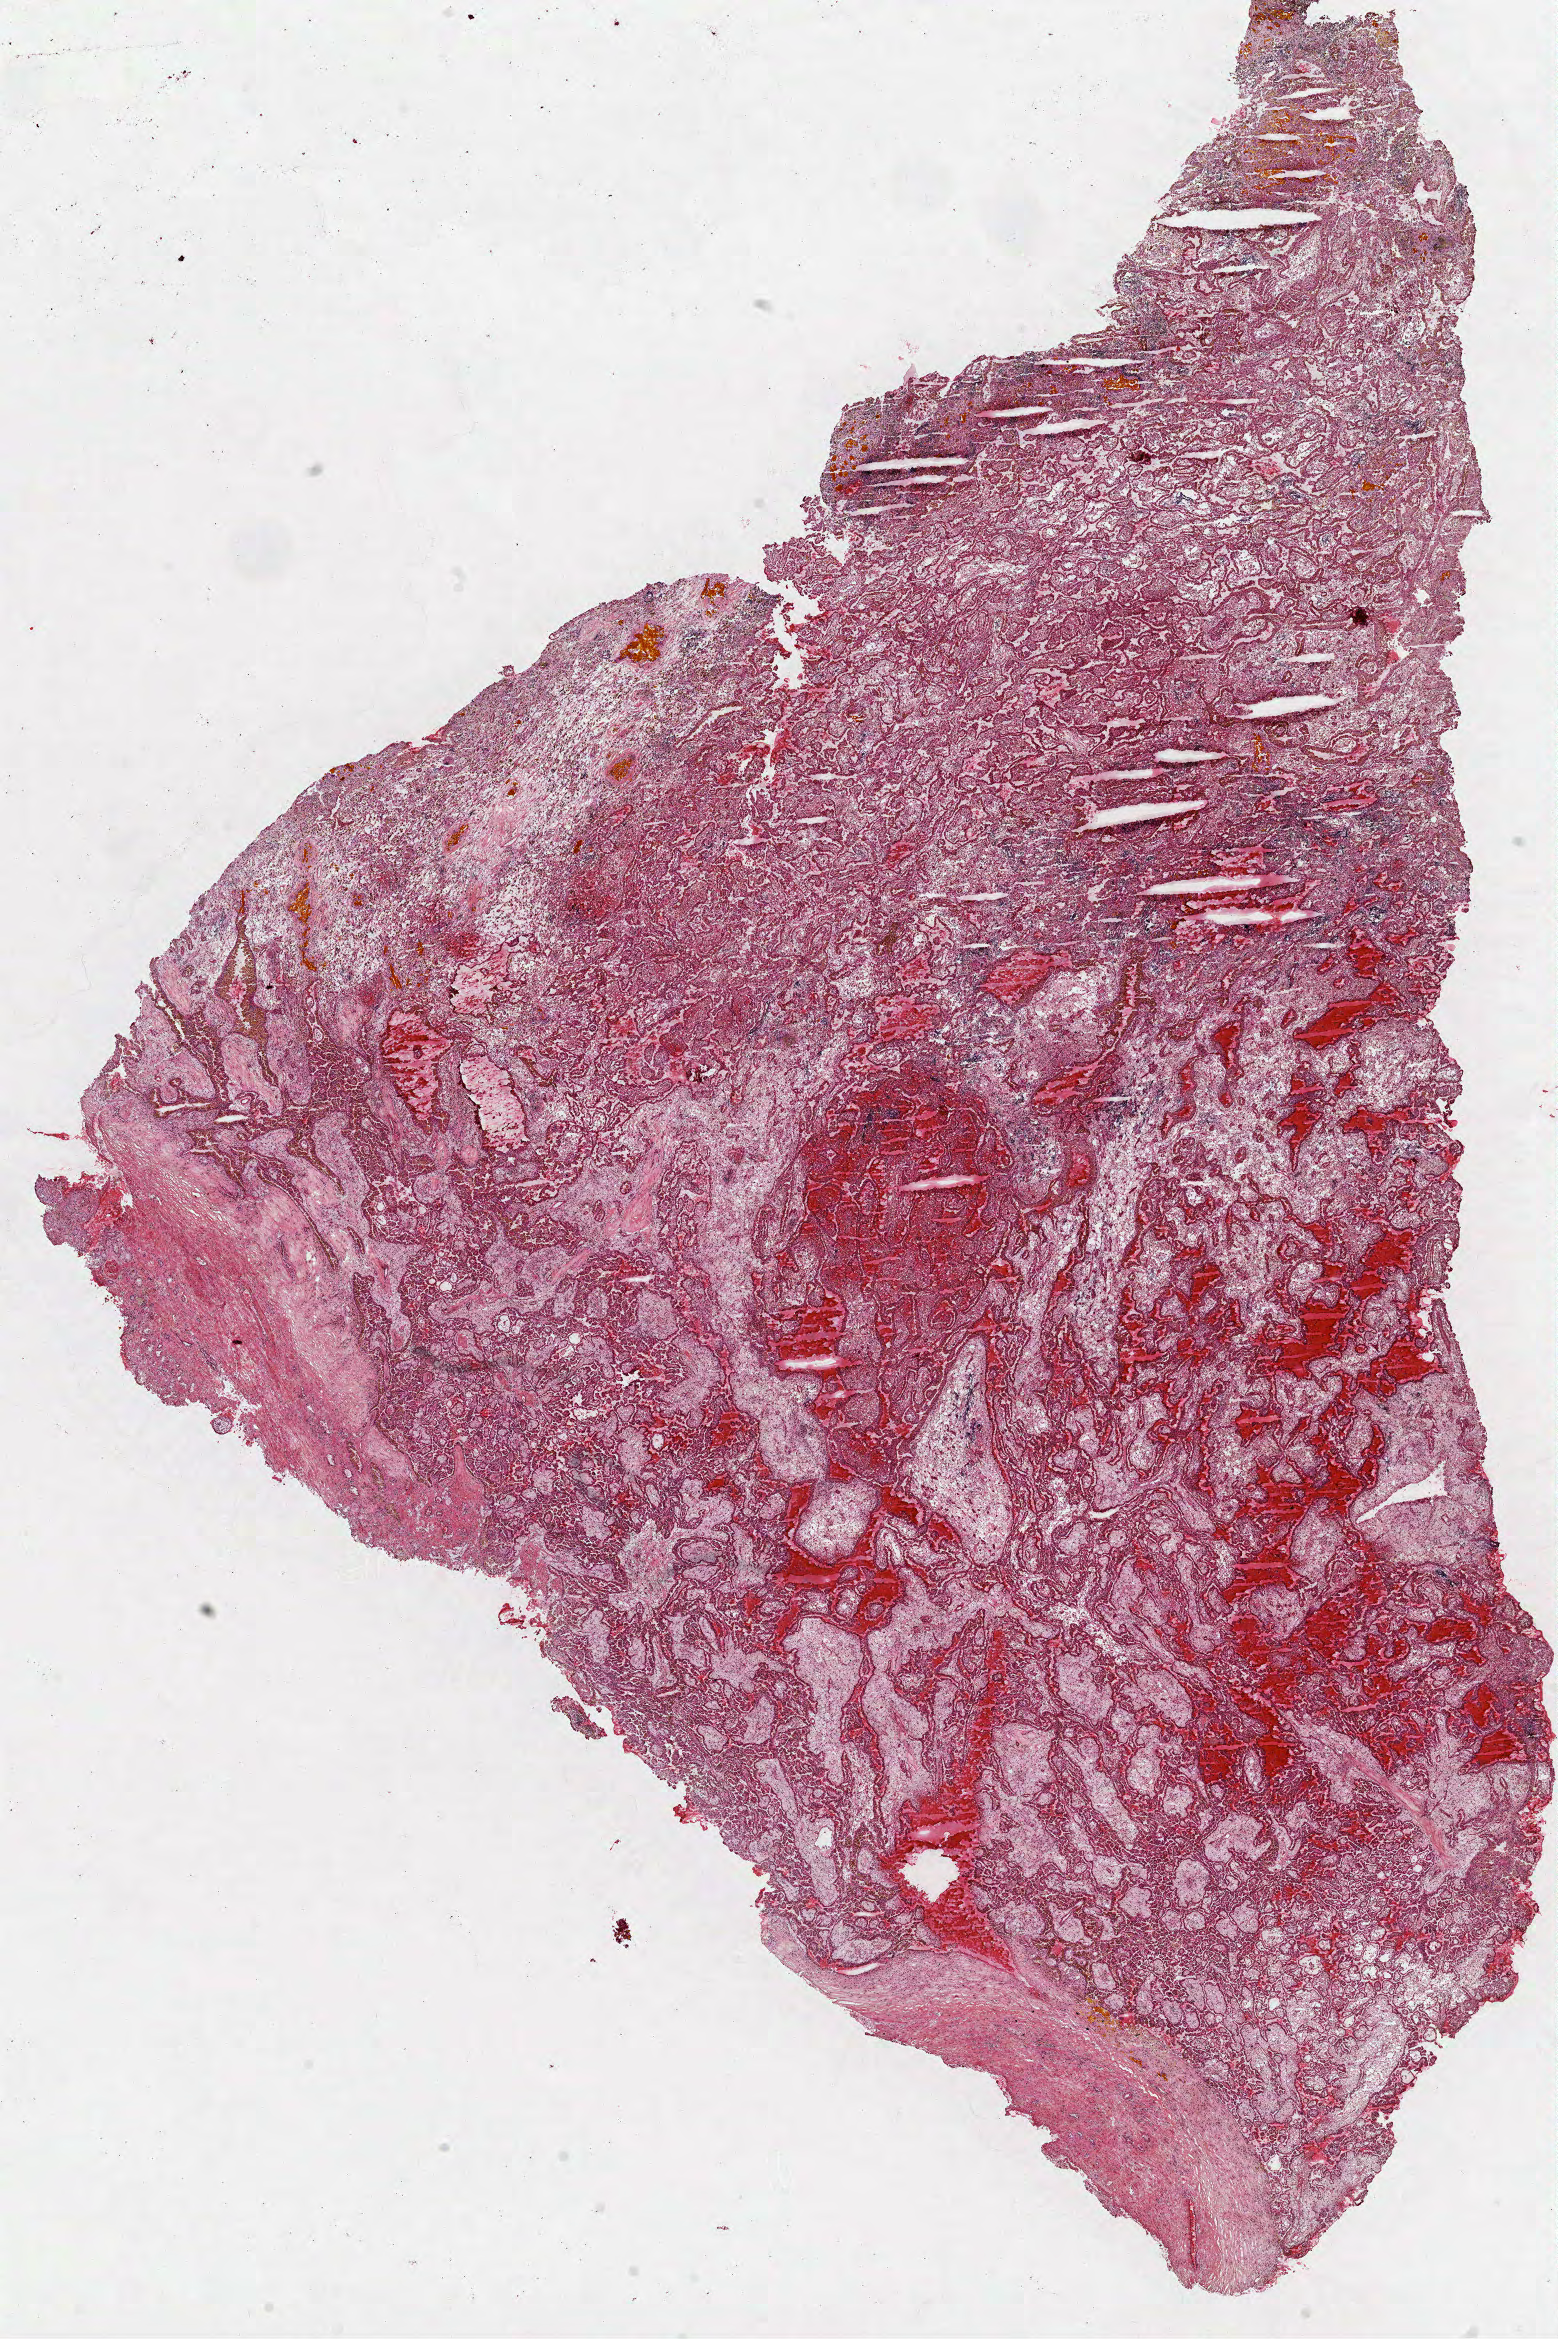
Digitized H&E-stained tissue section (whole slide), low-resolution overview of the scanned area, about 12.6 x 18.9 mm (from a 40x scan). Frozen section. Sample: primary tumour, kidney. Male patient; age at initial diagnosis 71 years. Composition of this section per pathologist review: tumour cells 100%, tumour nuclei 70%, normal cells 0%, stromal cells 0%, necrosis 0%. Infiltration values recorded for this section: lymphocyte infiltration 2%, monocyte infiltration 20%, neutrophil infiltration 0%.
Laterality: right. AJCC pathologic stage: I (7th edition). Histologic diagnosis: Papillary adenocarcinoma, NOS.